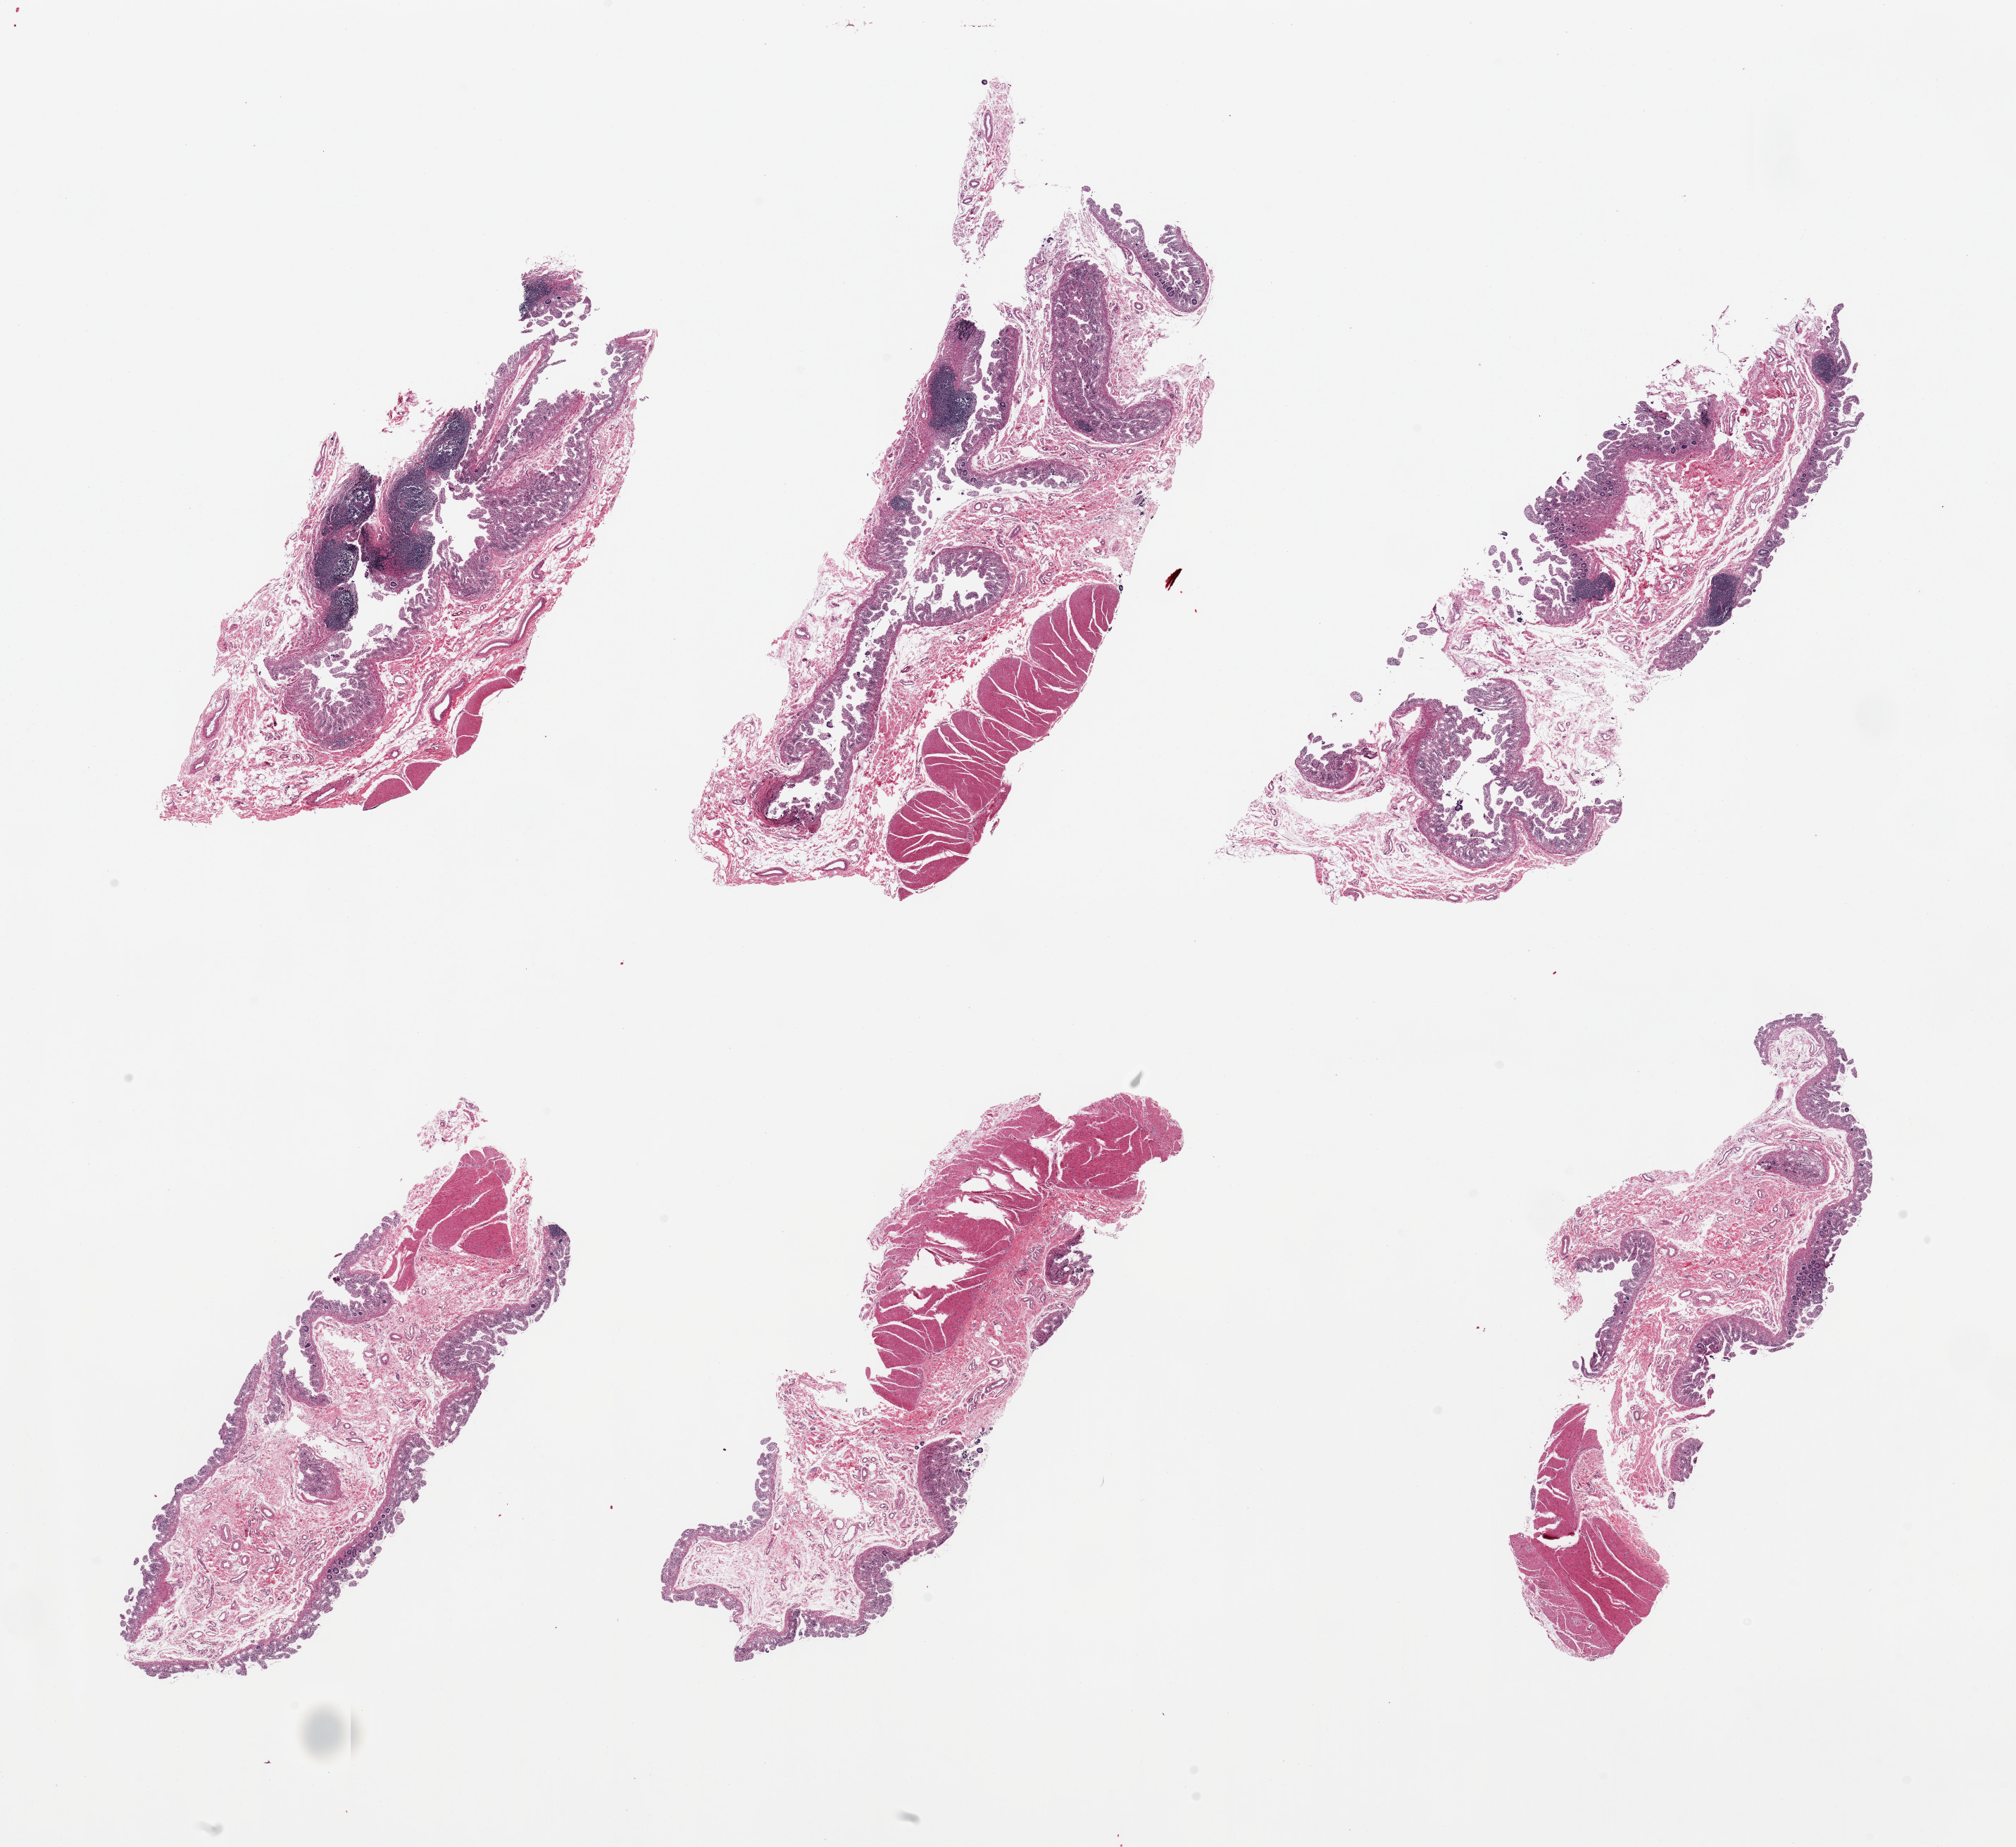
Haematoxylin and eosin whole-slide image, brightfield — whole scanned area (about 22.6 x 20.7 mm) shown as a low-resolution overview. PAXgene-fixed paraffin-embedded (PFPE) section. Section of ileum (target tissue). Tissue donor sample.
Review note (as recorded): 6 pieces, target lymphoid aggregates are ~5-10%.